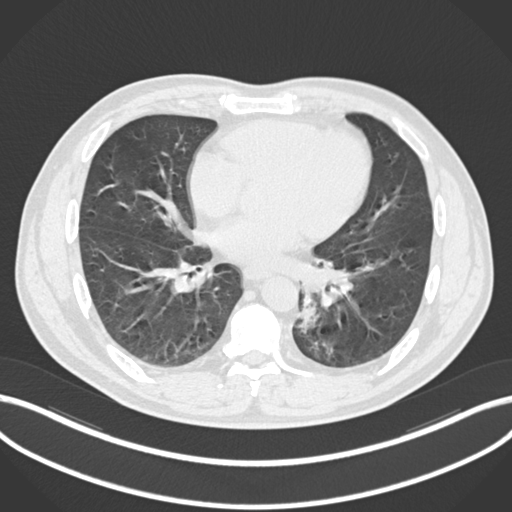
Chest CT, one axial slice; position 93 of 223 along the scan axis; 120 kVp; lung window (W 1500 / L -600 HU); 1 mm slice thickness; 512 × 512 image matrix, field of view 400 × 400 mm. Patient: male, 50 years. From the clinical record (not read from this slice): clinical TNM (as recorded): T2a N3 M0.
Structures marked on this image (rectangle marked by the reading radiologist):
- lung tumour (recorded histology: squamous cell carcinoma): bounding box [x1, y1, x2, y2] px = [296, 300, 320, 335]